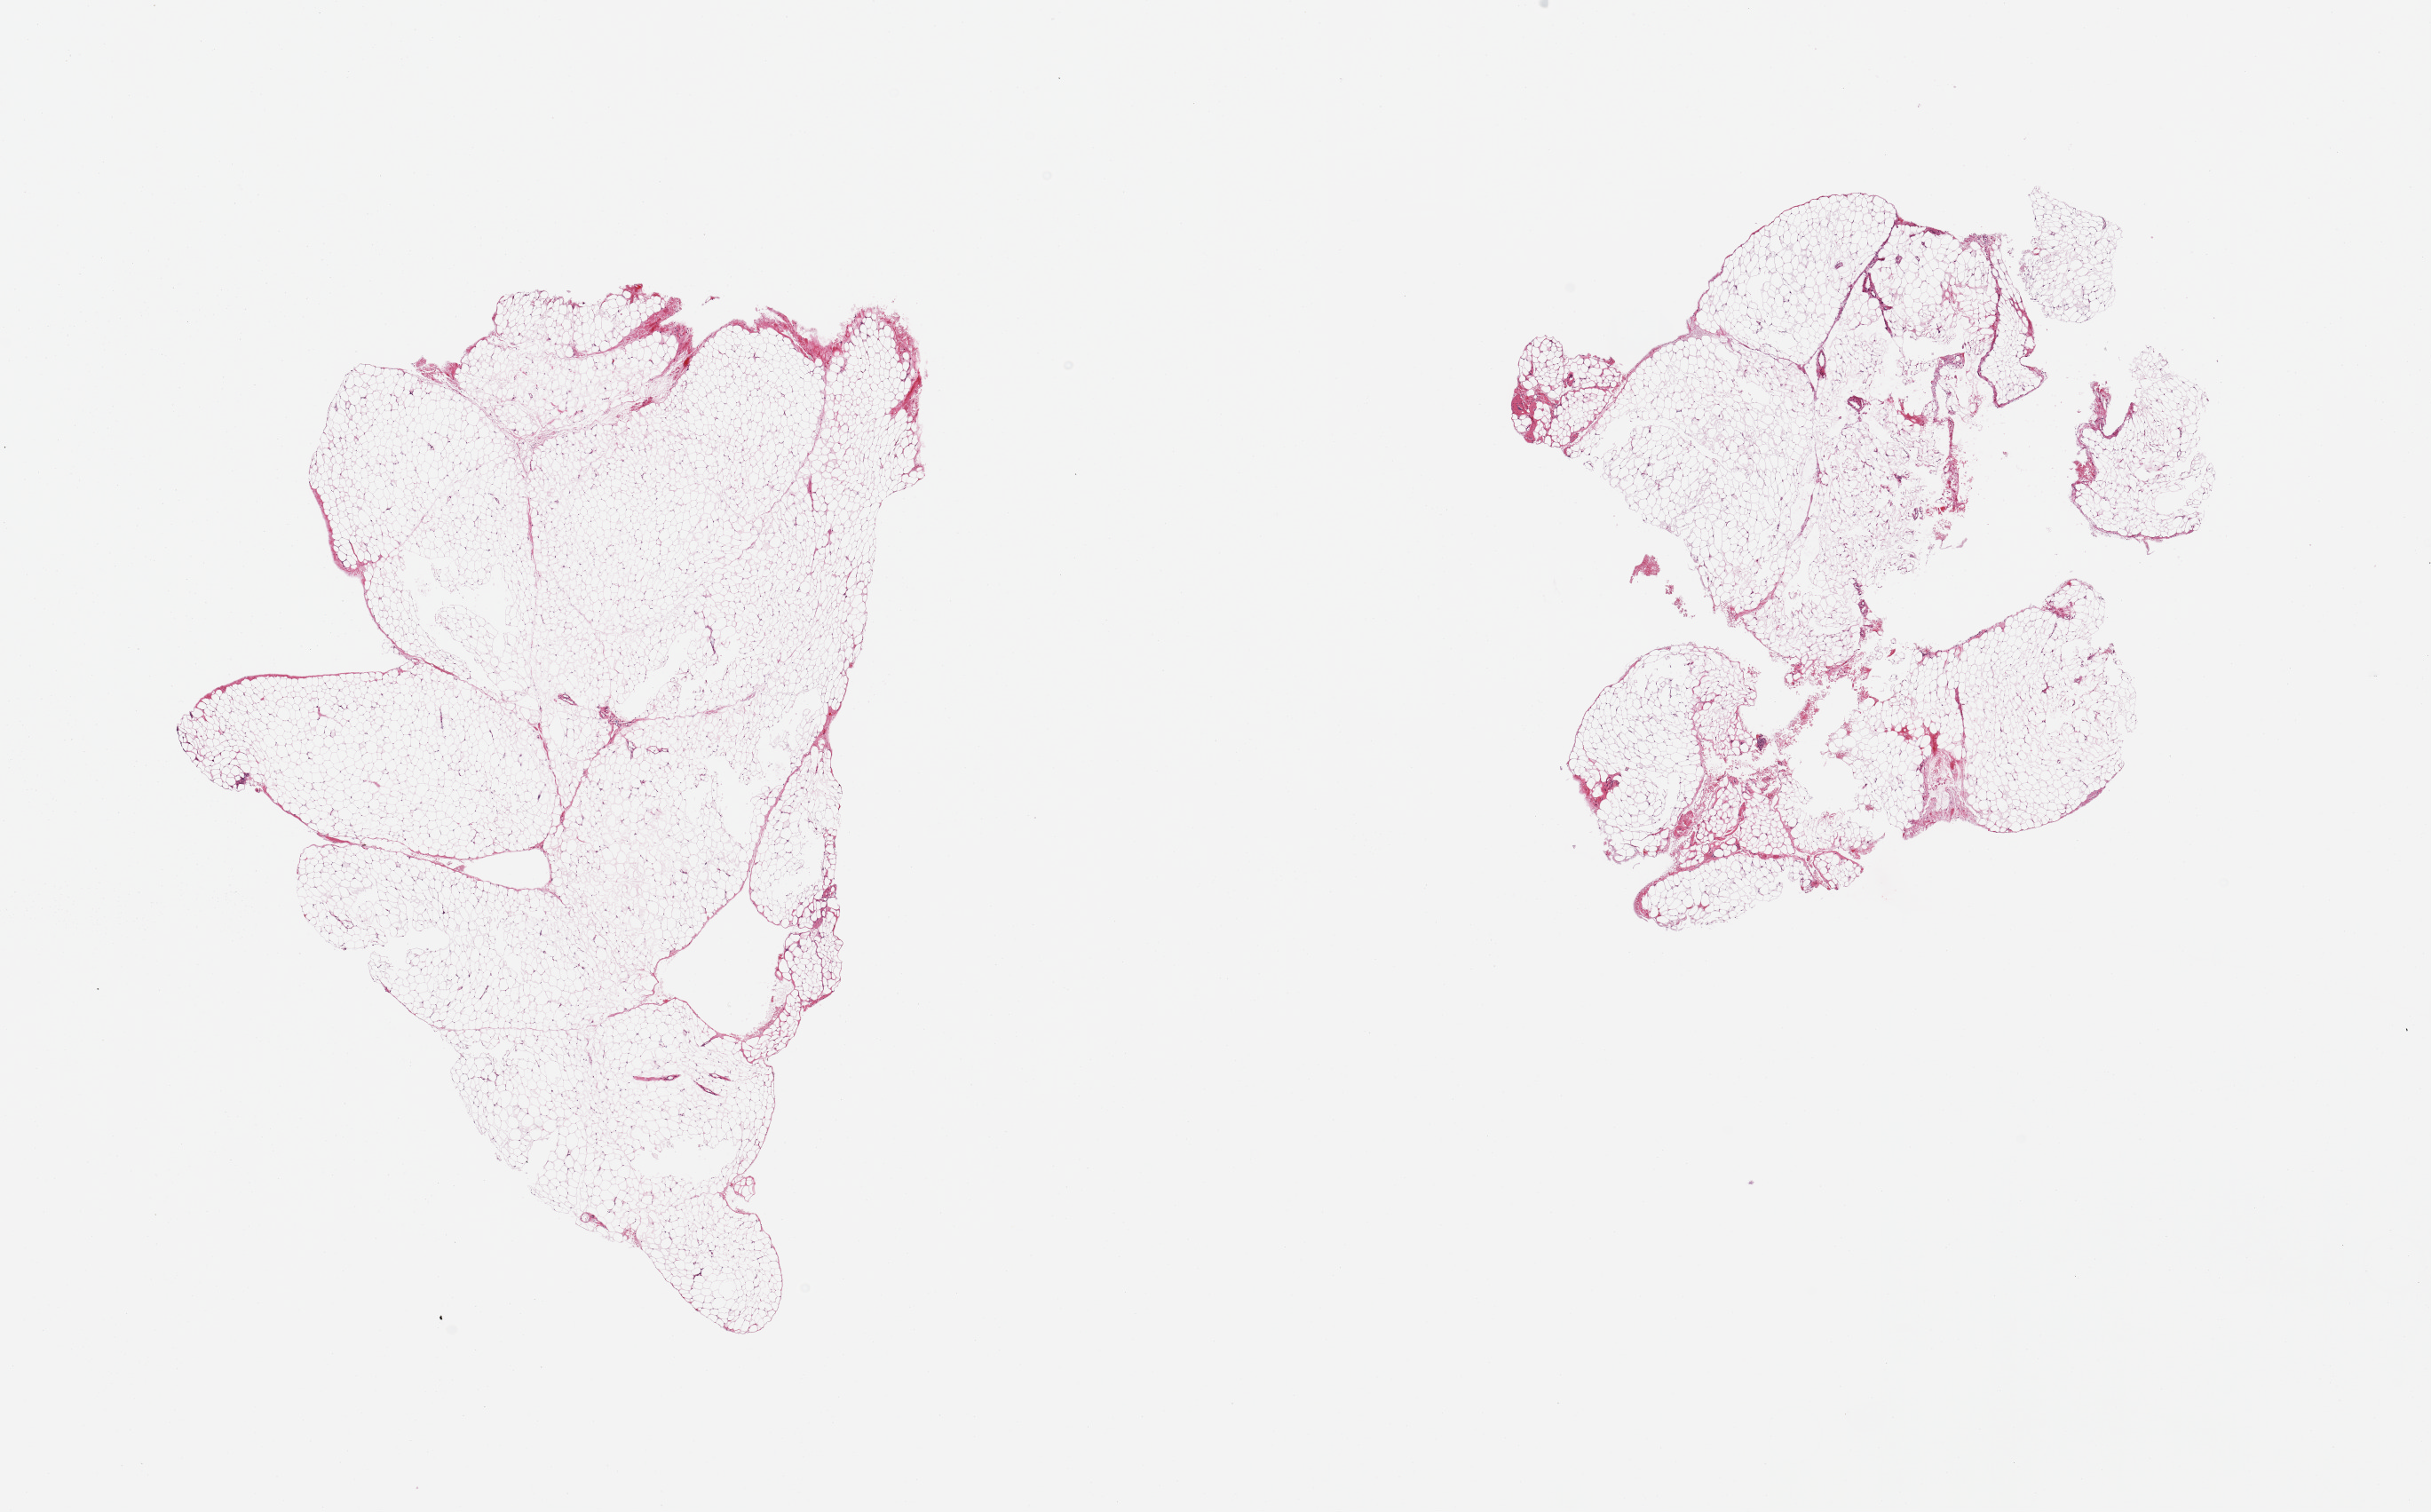
Digitized hematoxylin and eosin (H&E)-stained section, whole scanned area (about 21.7 x 13.5 mm, slide scanned at 20x) shown as a low-resolution overview, PAXgene-fixed paraffin-embedded (PFPE) section, target tissue: omentum, tissue donor sample. Donor sex: male.
Pathologist's review note for this sample: 2 pieces; lobulated adipose tissue.